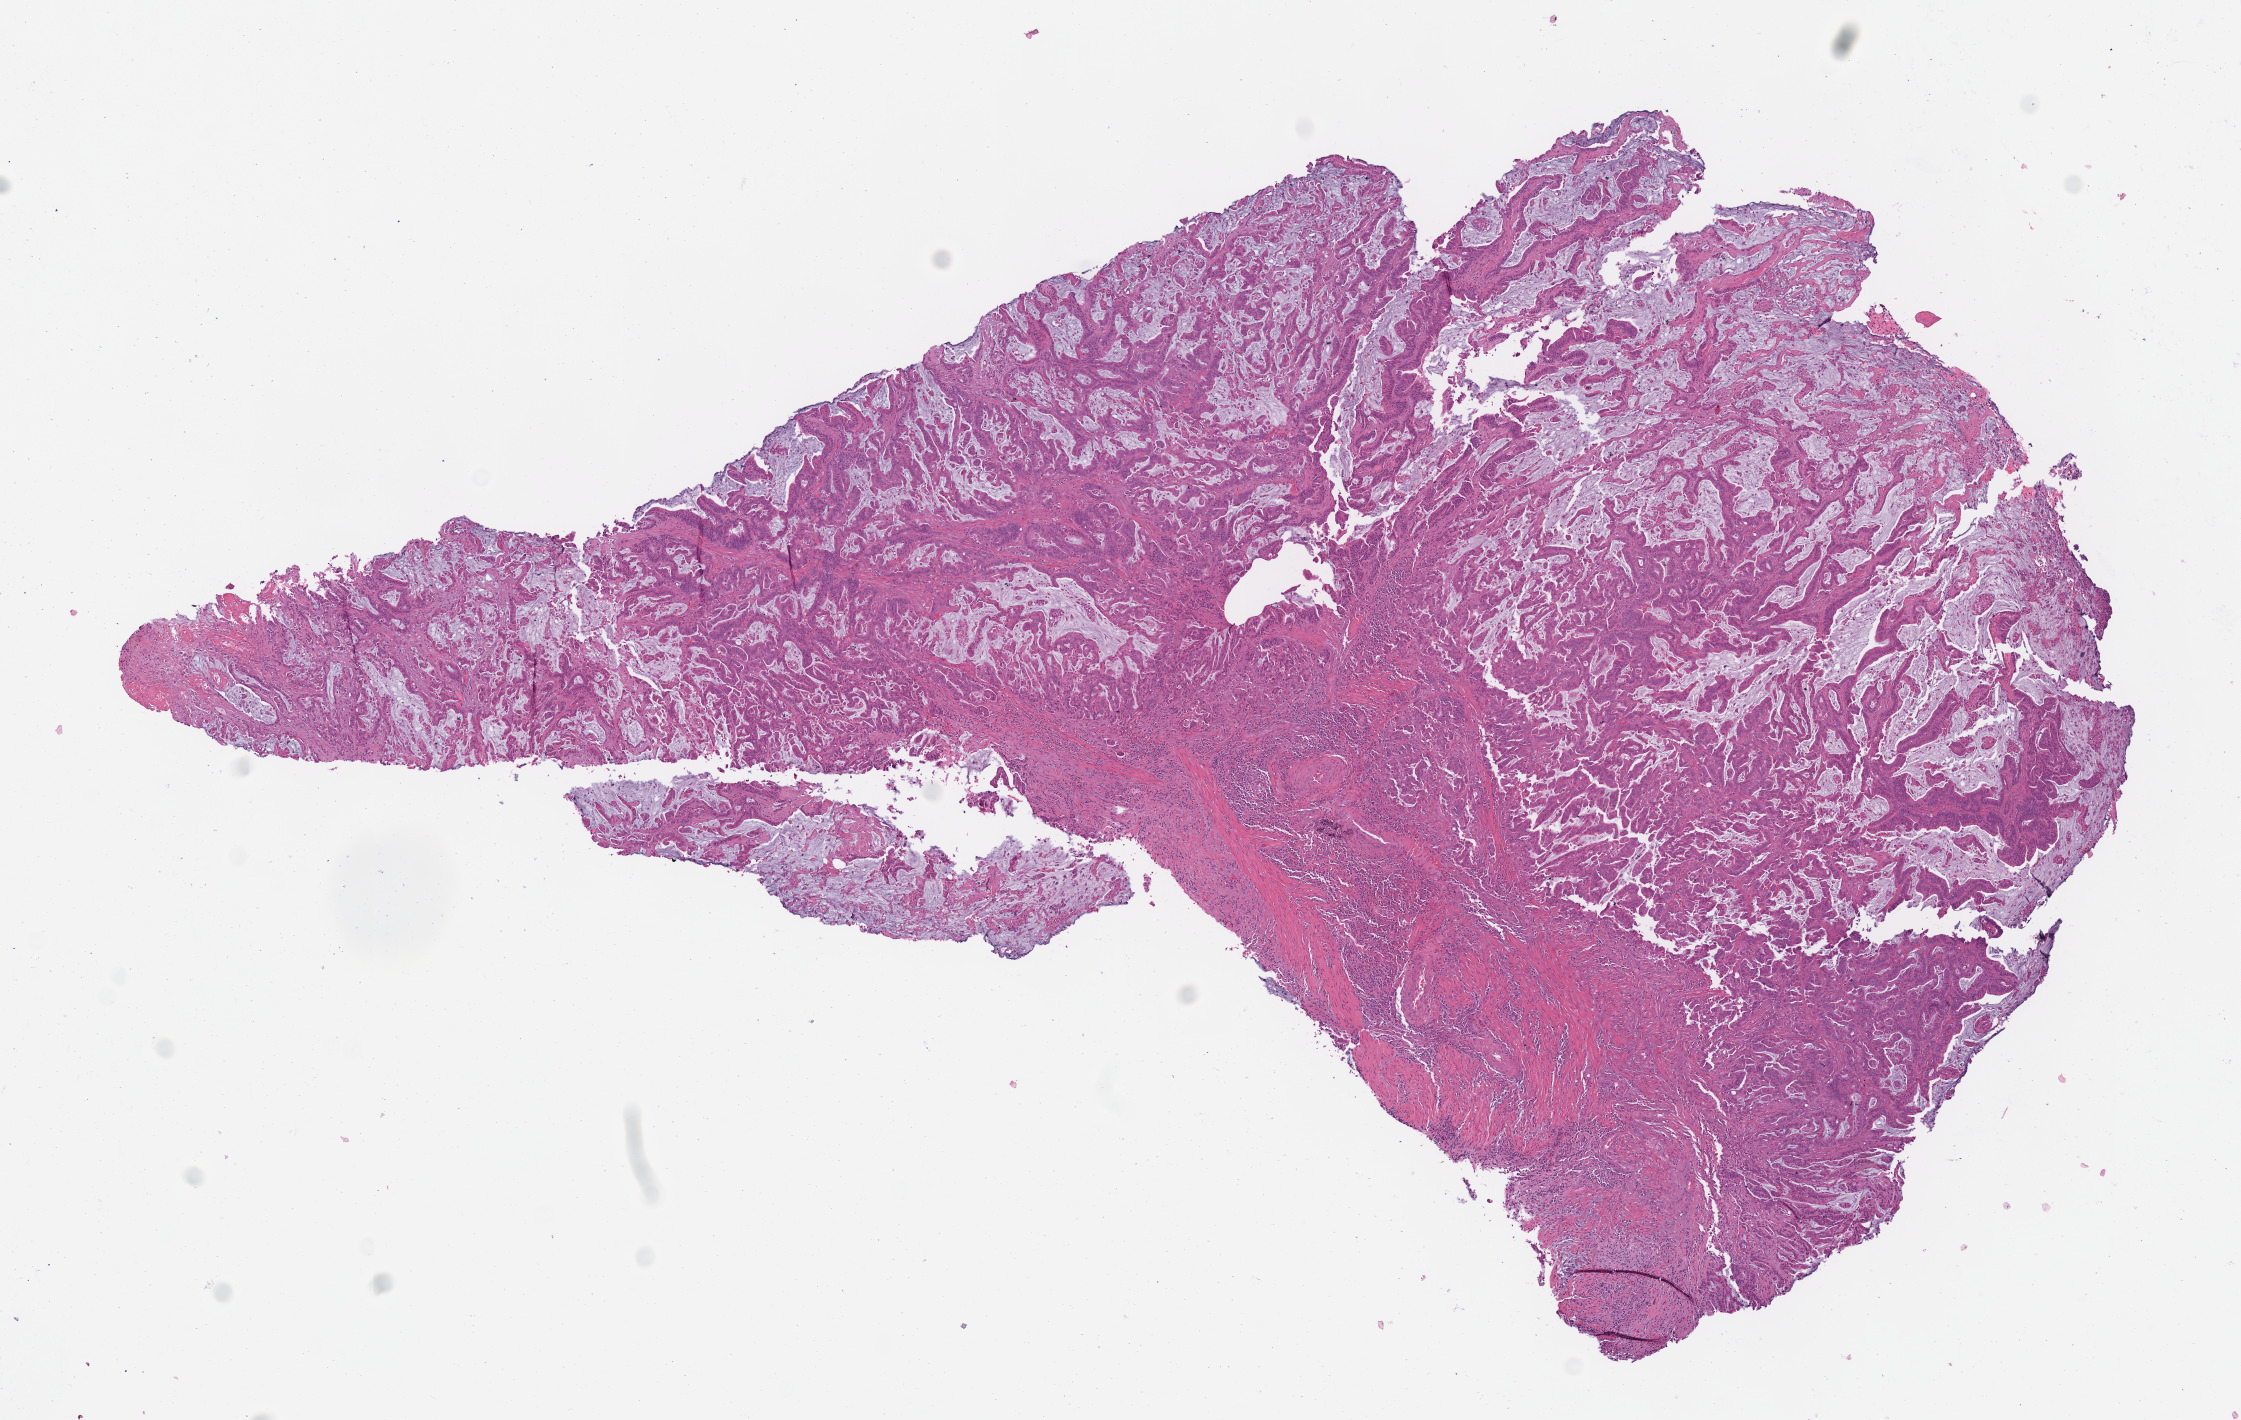
Digitized H&E tissue section (whole slide) — low-resolution overview of the scanned area, about 8.8 x 5.6 mm, frozen section from the top of the tissue portion, colon, primary tumour sample. Patient: female, age at initial diagnosis 84 years. Slide review estimates, as recorded: tumour cells 65%, tumour nuclei 80%, normal cells 0%, stromal cells 20%, necrosis 15%. Inflammatory infiltration, as recorded: lymphocyte infiltration 10%, monocyte infiltration 0%, neutrophil infiltration 0%.
Histologic diagnosis: Adenocarcinoma, NOS (ascending colon). TNM: T3 N0 M0. AJCC pathologic stage: IIA. Lymph nodes positive (case pathology): 0 of 25 examined.